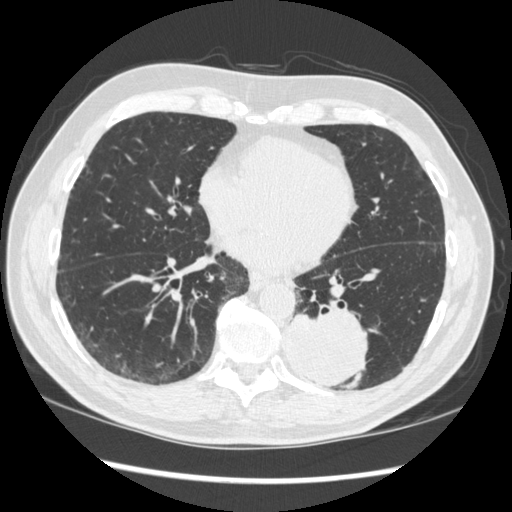
Axial slice from a low-dose chest CT screening exam. Baseline annual screen. Lung window (W 1500 / L -600 HU). 1.25 mm slice thickness. Slice 130 of 348 in the series. 512 × 512 image matrix, field of view 360 × 360 mm. Male participant, aged 72 years at enrolment. Current smoker at enrolment.
• Lesion marked by an expert reader, bounding box (x1, y1, x2, y2) in pixels: (271, 298, 375, 387).
• The screening reader recorded 2 non-calcified nodules or masses ≥4 mm on this exam; which of them this box marks is not recorded.
• Participant outcome: lung cancer diagnosed 37 days after this screen — squamous cell carcinoma, NOS, left lower lobe, stage IIIA (AJCC 6th edition), 60 mm at pathology.